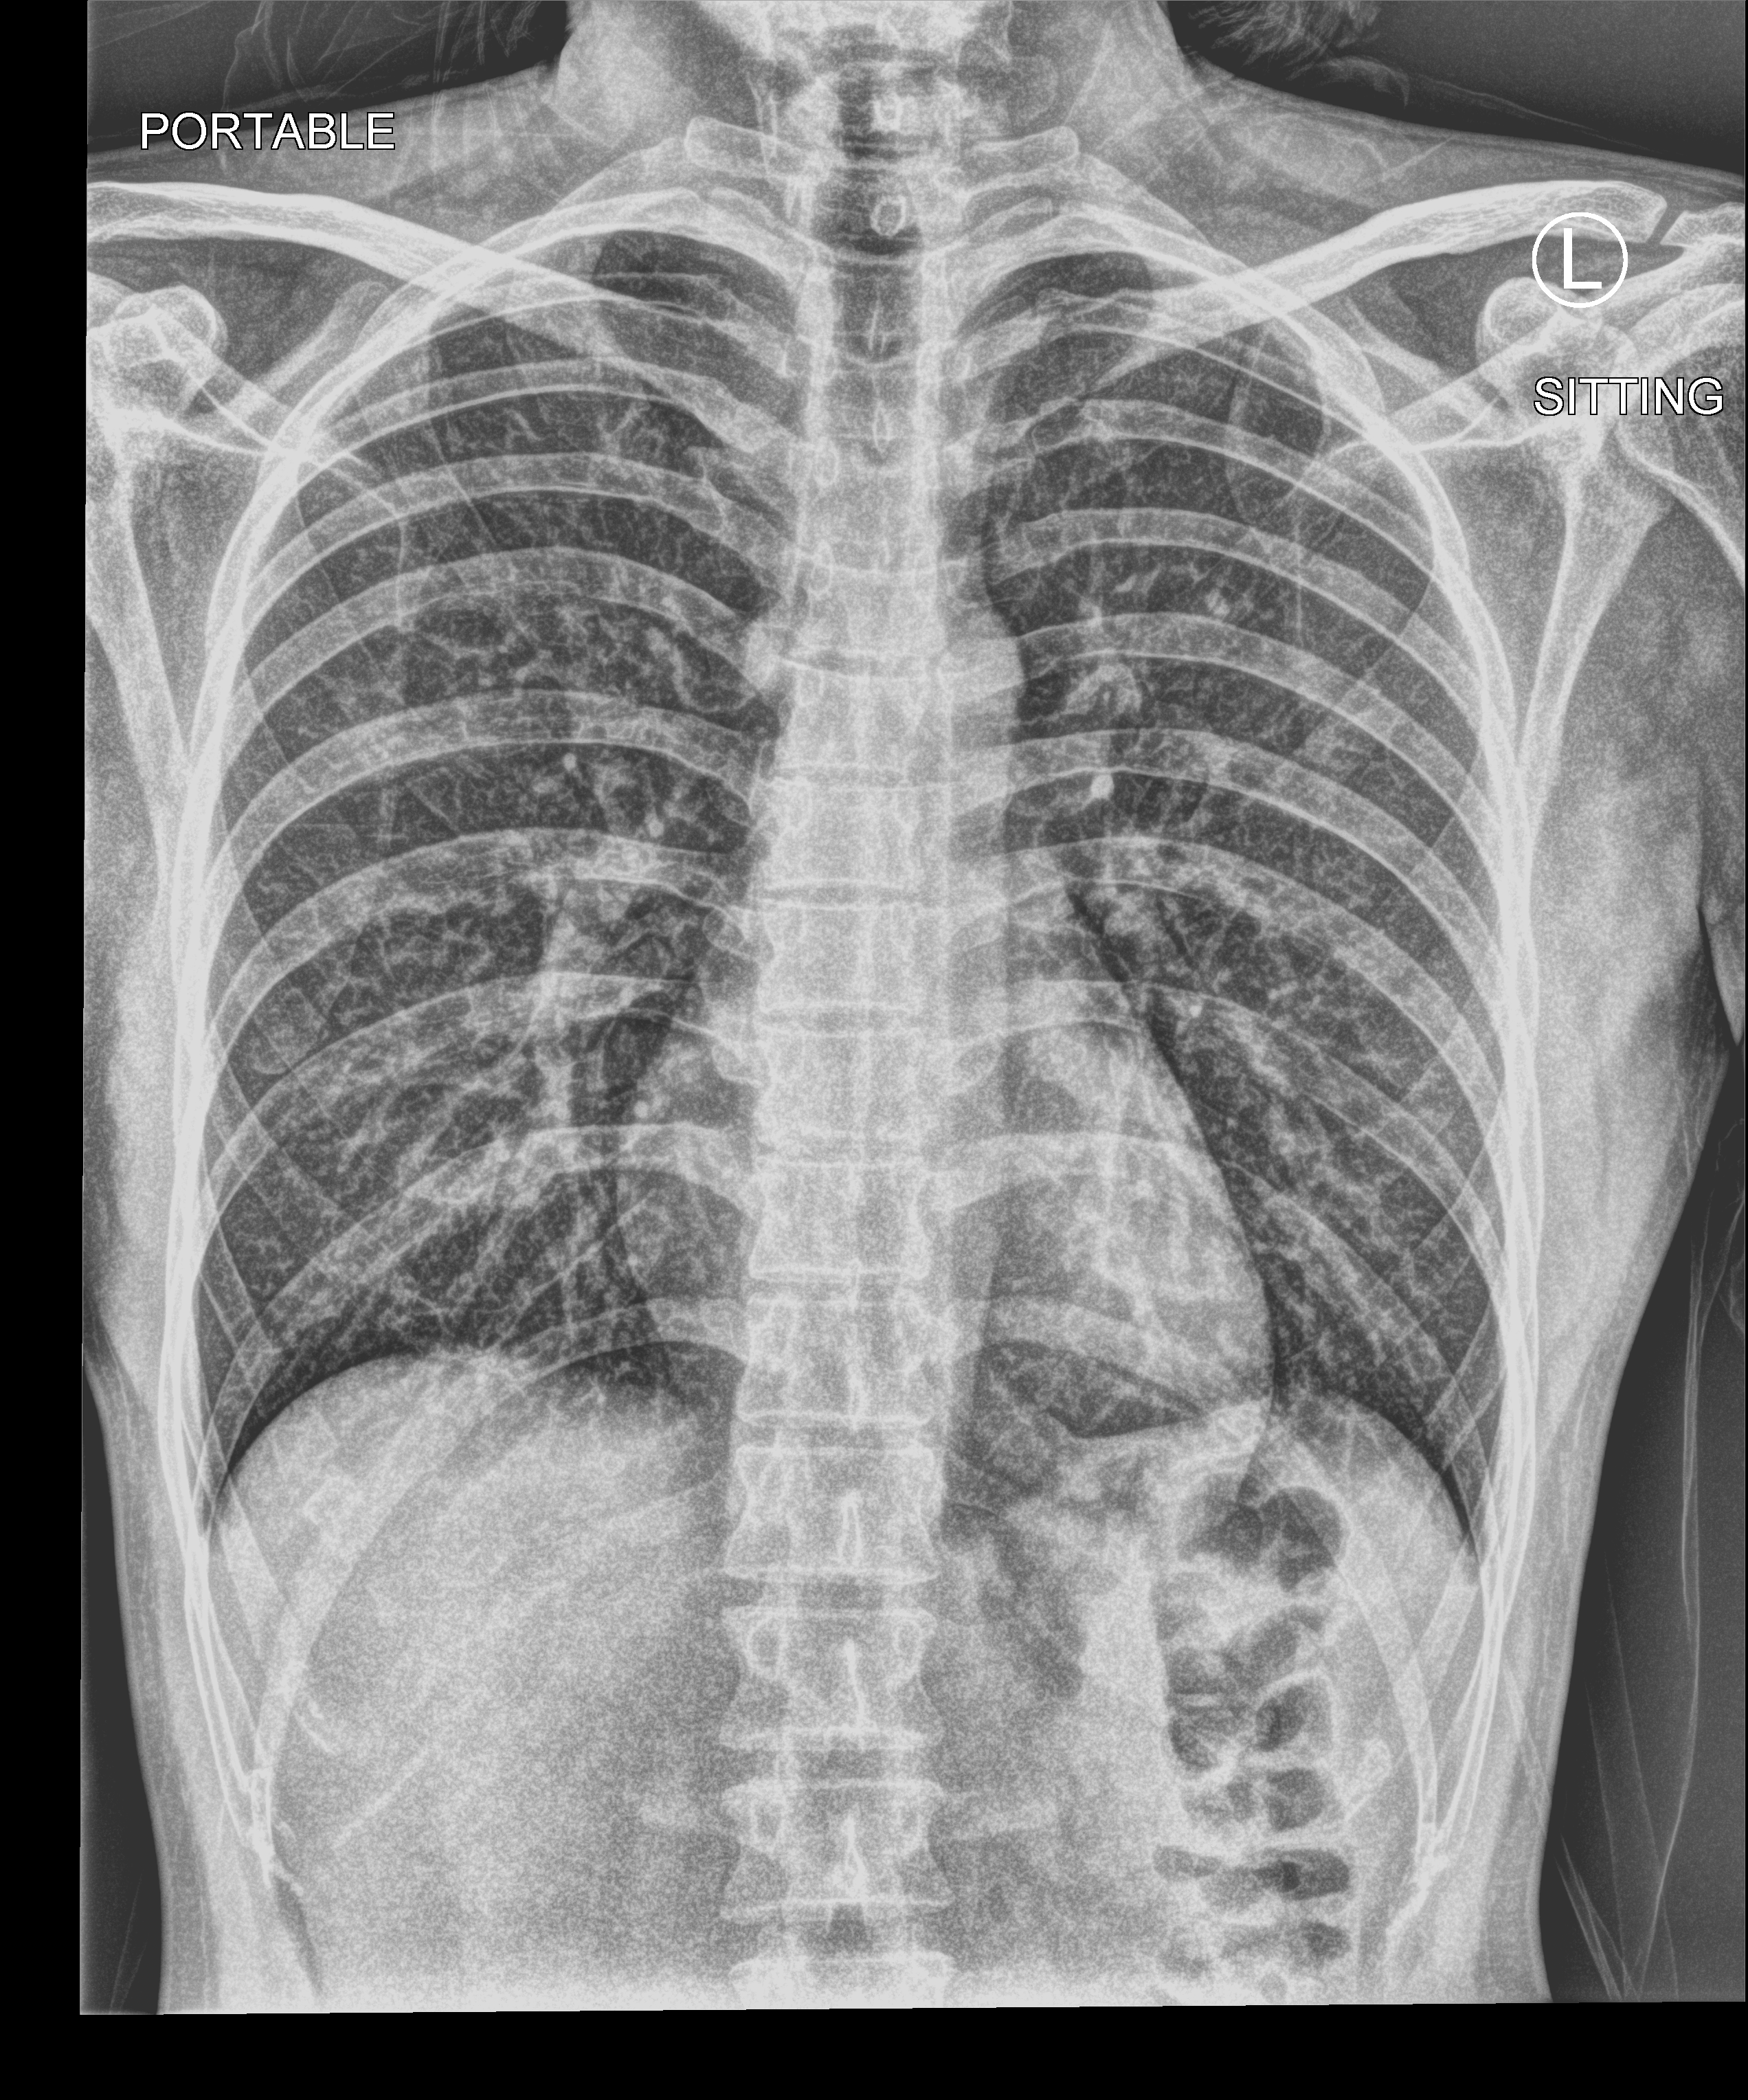
Portable chest radiograph; anteroposterior (AP) projection. Patient hospitalised with COVID-19; male, aged 18–59 years.
From the hospital-stay record, not from the radiograph (when in the stay this image was taken is not recorded):
- chronic kidney disease (admission record): no
- mechanically ventilated during this hospital stay: no